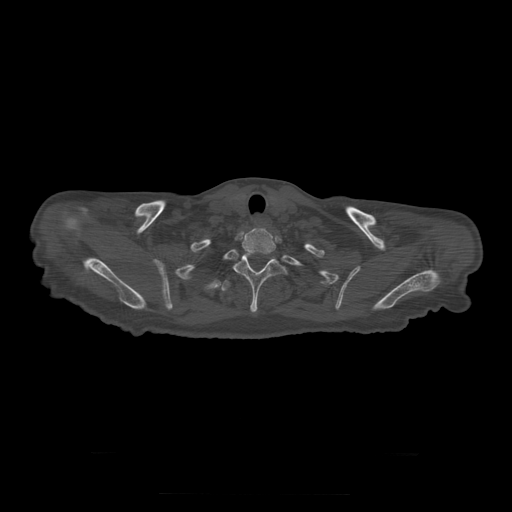
CT including the spine, one axial slice. Position 277 of 397 along the scan axis. Reconstruction kernel STANDARD. 120 kVp. Bone window (W 1800 / L 400 HU). 1.25 mm slice thickness. 512 × 512 image matrix, field of view 510 × 510 mm. Patient age 73 years. From the clinical record (not read from this slice): primary cancer: prostate.
Annotated regions visible in this slice (semi-automatic segmentation, software-assisted and operator-edited):
- T1 vertebra: bounding box (x1, y1, x2, y2) in pixels: (240, 231, 276, 254)
- T2 vertebra: (233, 253, 288, 313)
- T3 vertebra: (221, 280, 232, 292)